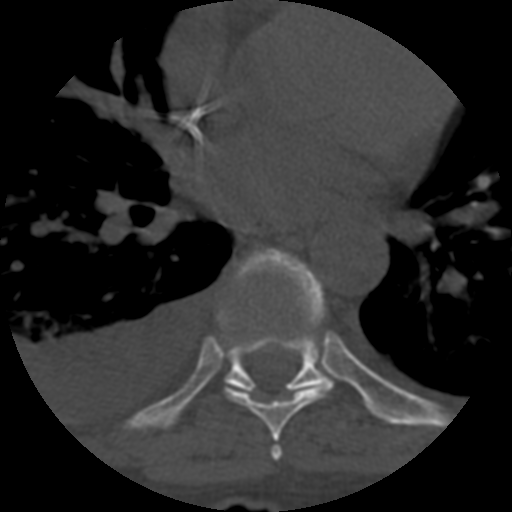
CT including the spine, one axial slice; slice 407 of 708 in the series (ordered by position); reconstruction kernel STANDARD; 120 kVp; one of 3 acquisitions stored at this slice position; bone window (W 1800 / L 400 HU); 512 × 512 image matrix. Patient age 55 years. Case-level facts recorded for this patient, not image findings: primary cancer: colon; vertebrae with lytic lesions (as recorded): T12, L1, L5.
Annotated regions visible in this slice (semi-automatic segmentation, software-assisted and operator-edited):
- T6 vertebra: bounding box <270,446,282,460> (left, top, right, bottom; pixels)
- T7 vertebra: <225,326,333,442>
- T8 vertebra: <219,249,327,396>